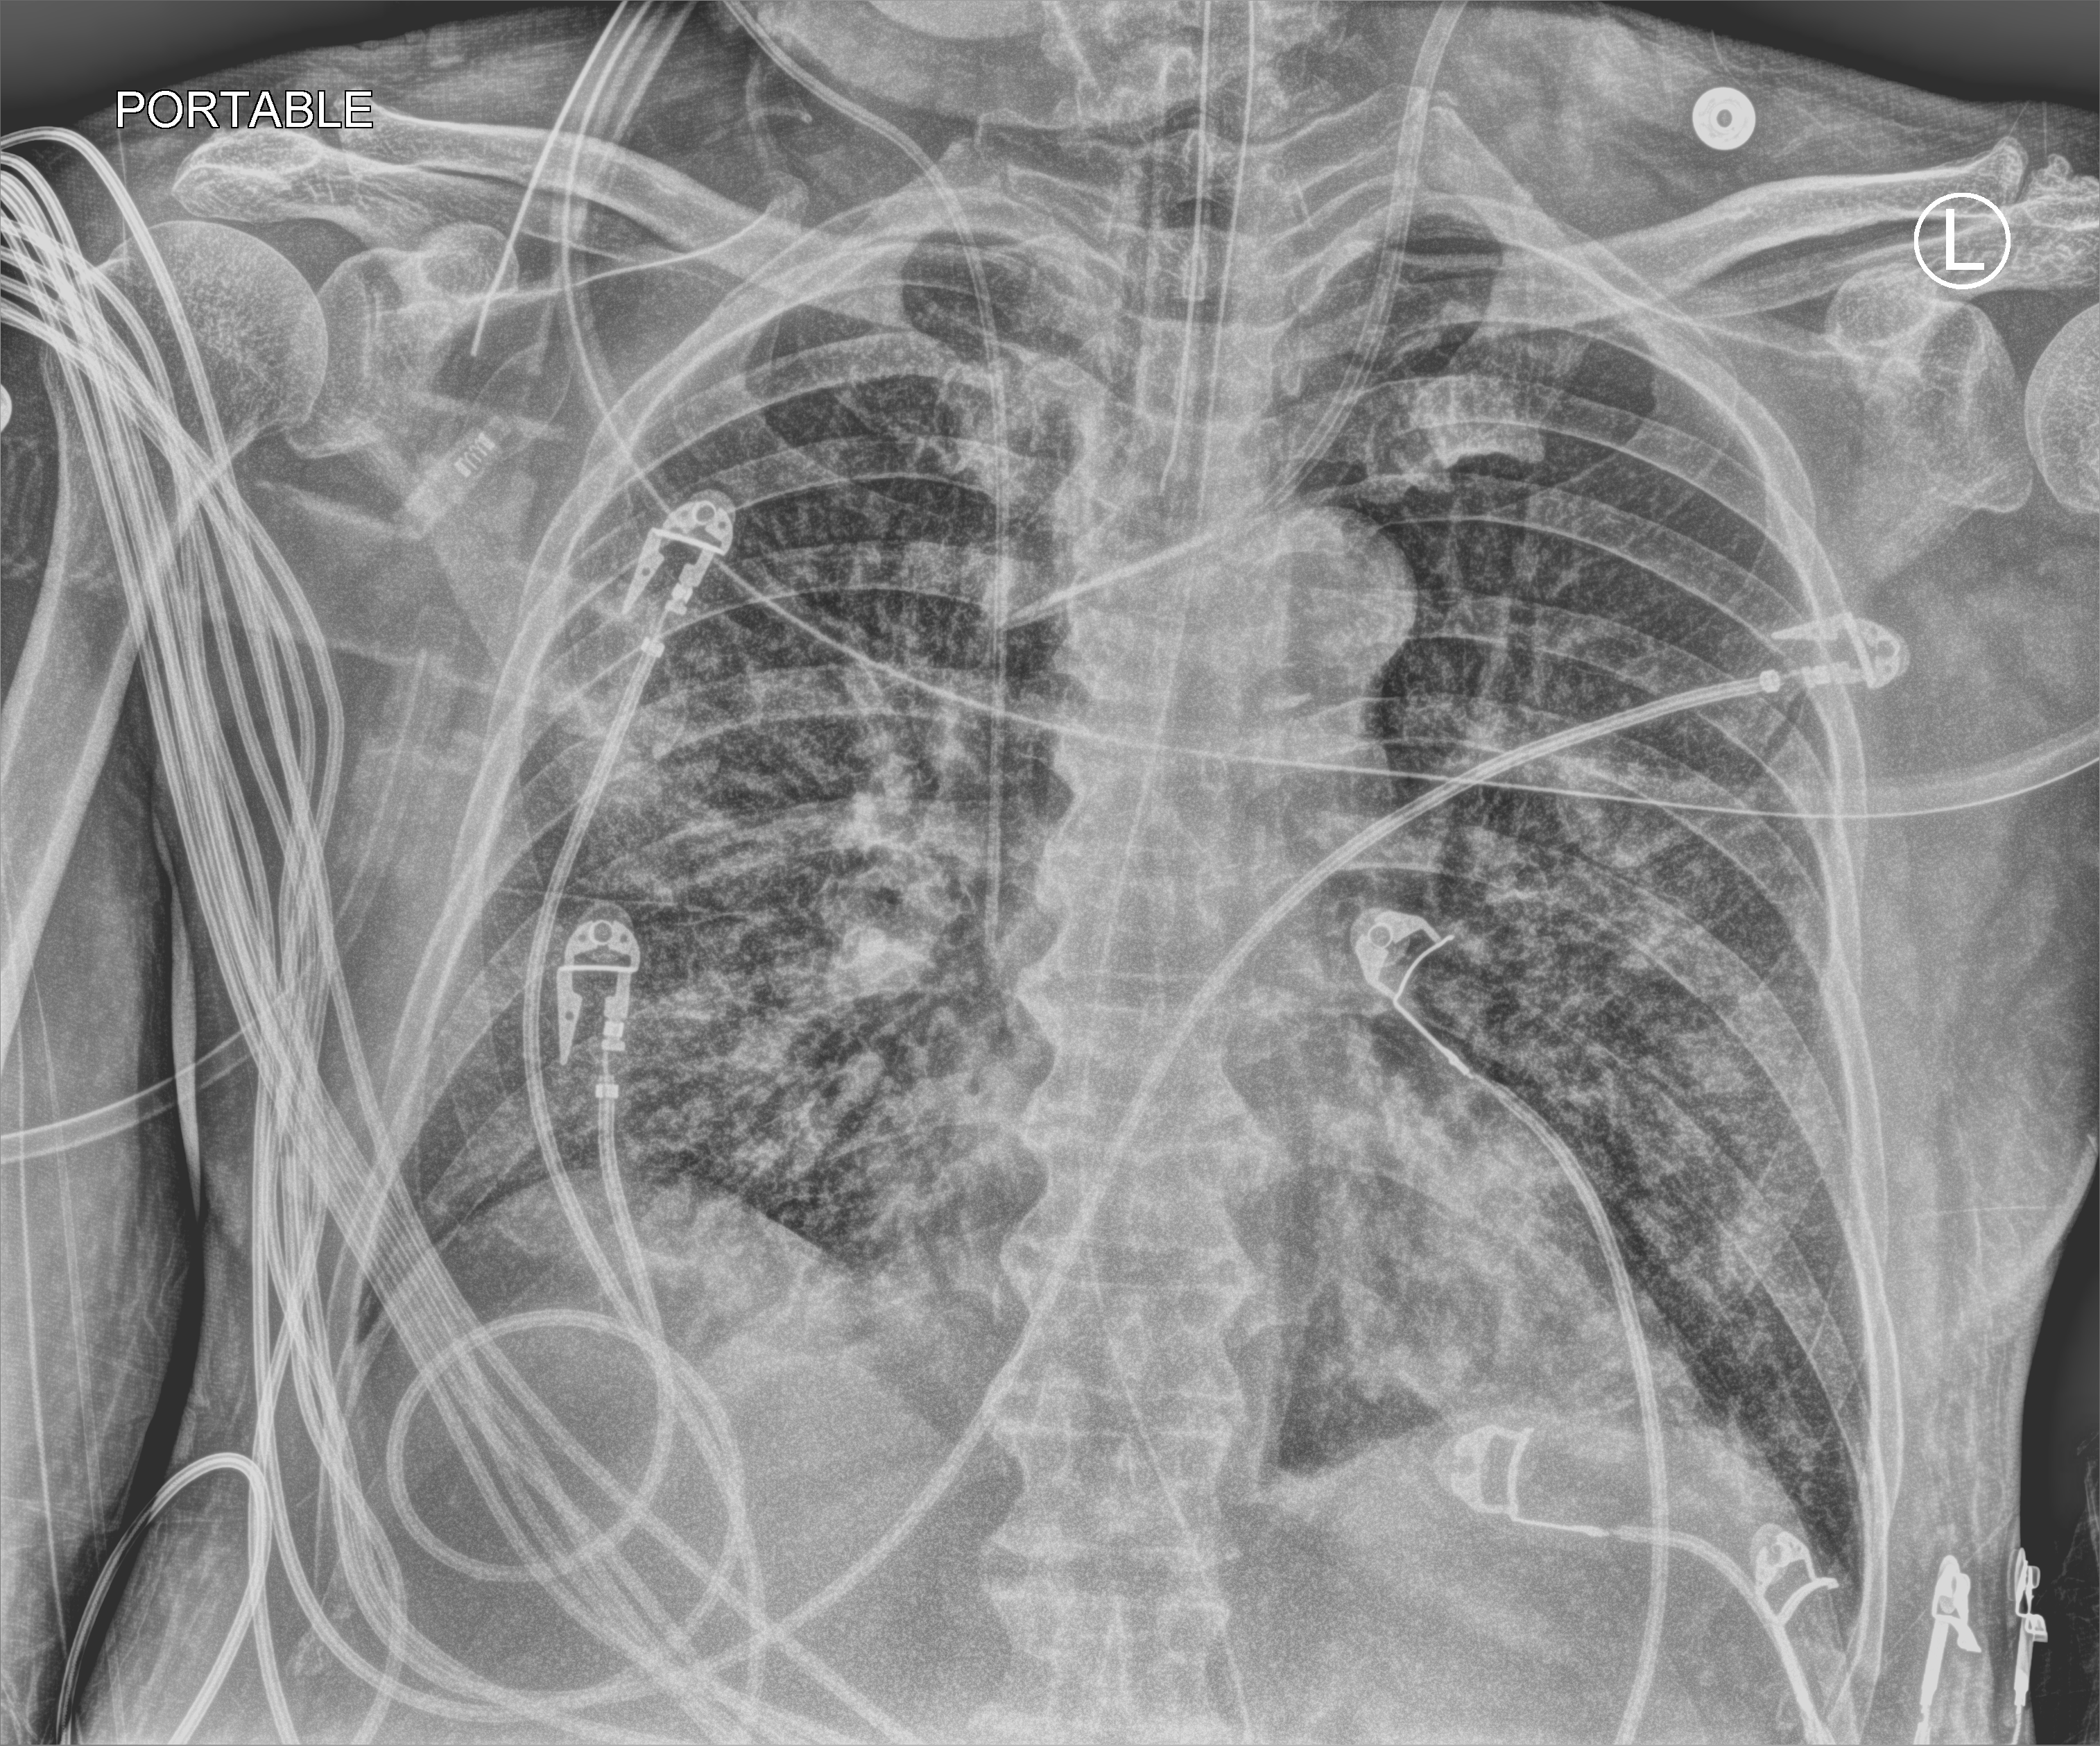
Chest X-ray (portable); anteroposterior (AP) projection. Patient hospitalised with COVID-19; male, aged 60–74 years.
Hospital-stay facts (about this admission, not read from this image; timing relative to this image not recorded): other chronic lung disease (admission record): no.